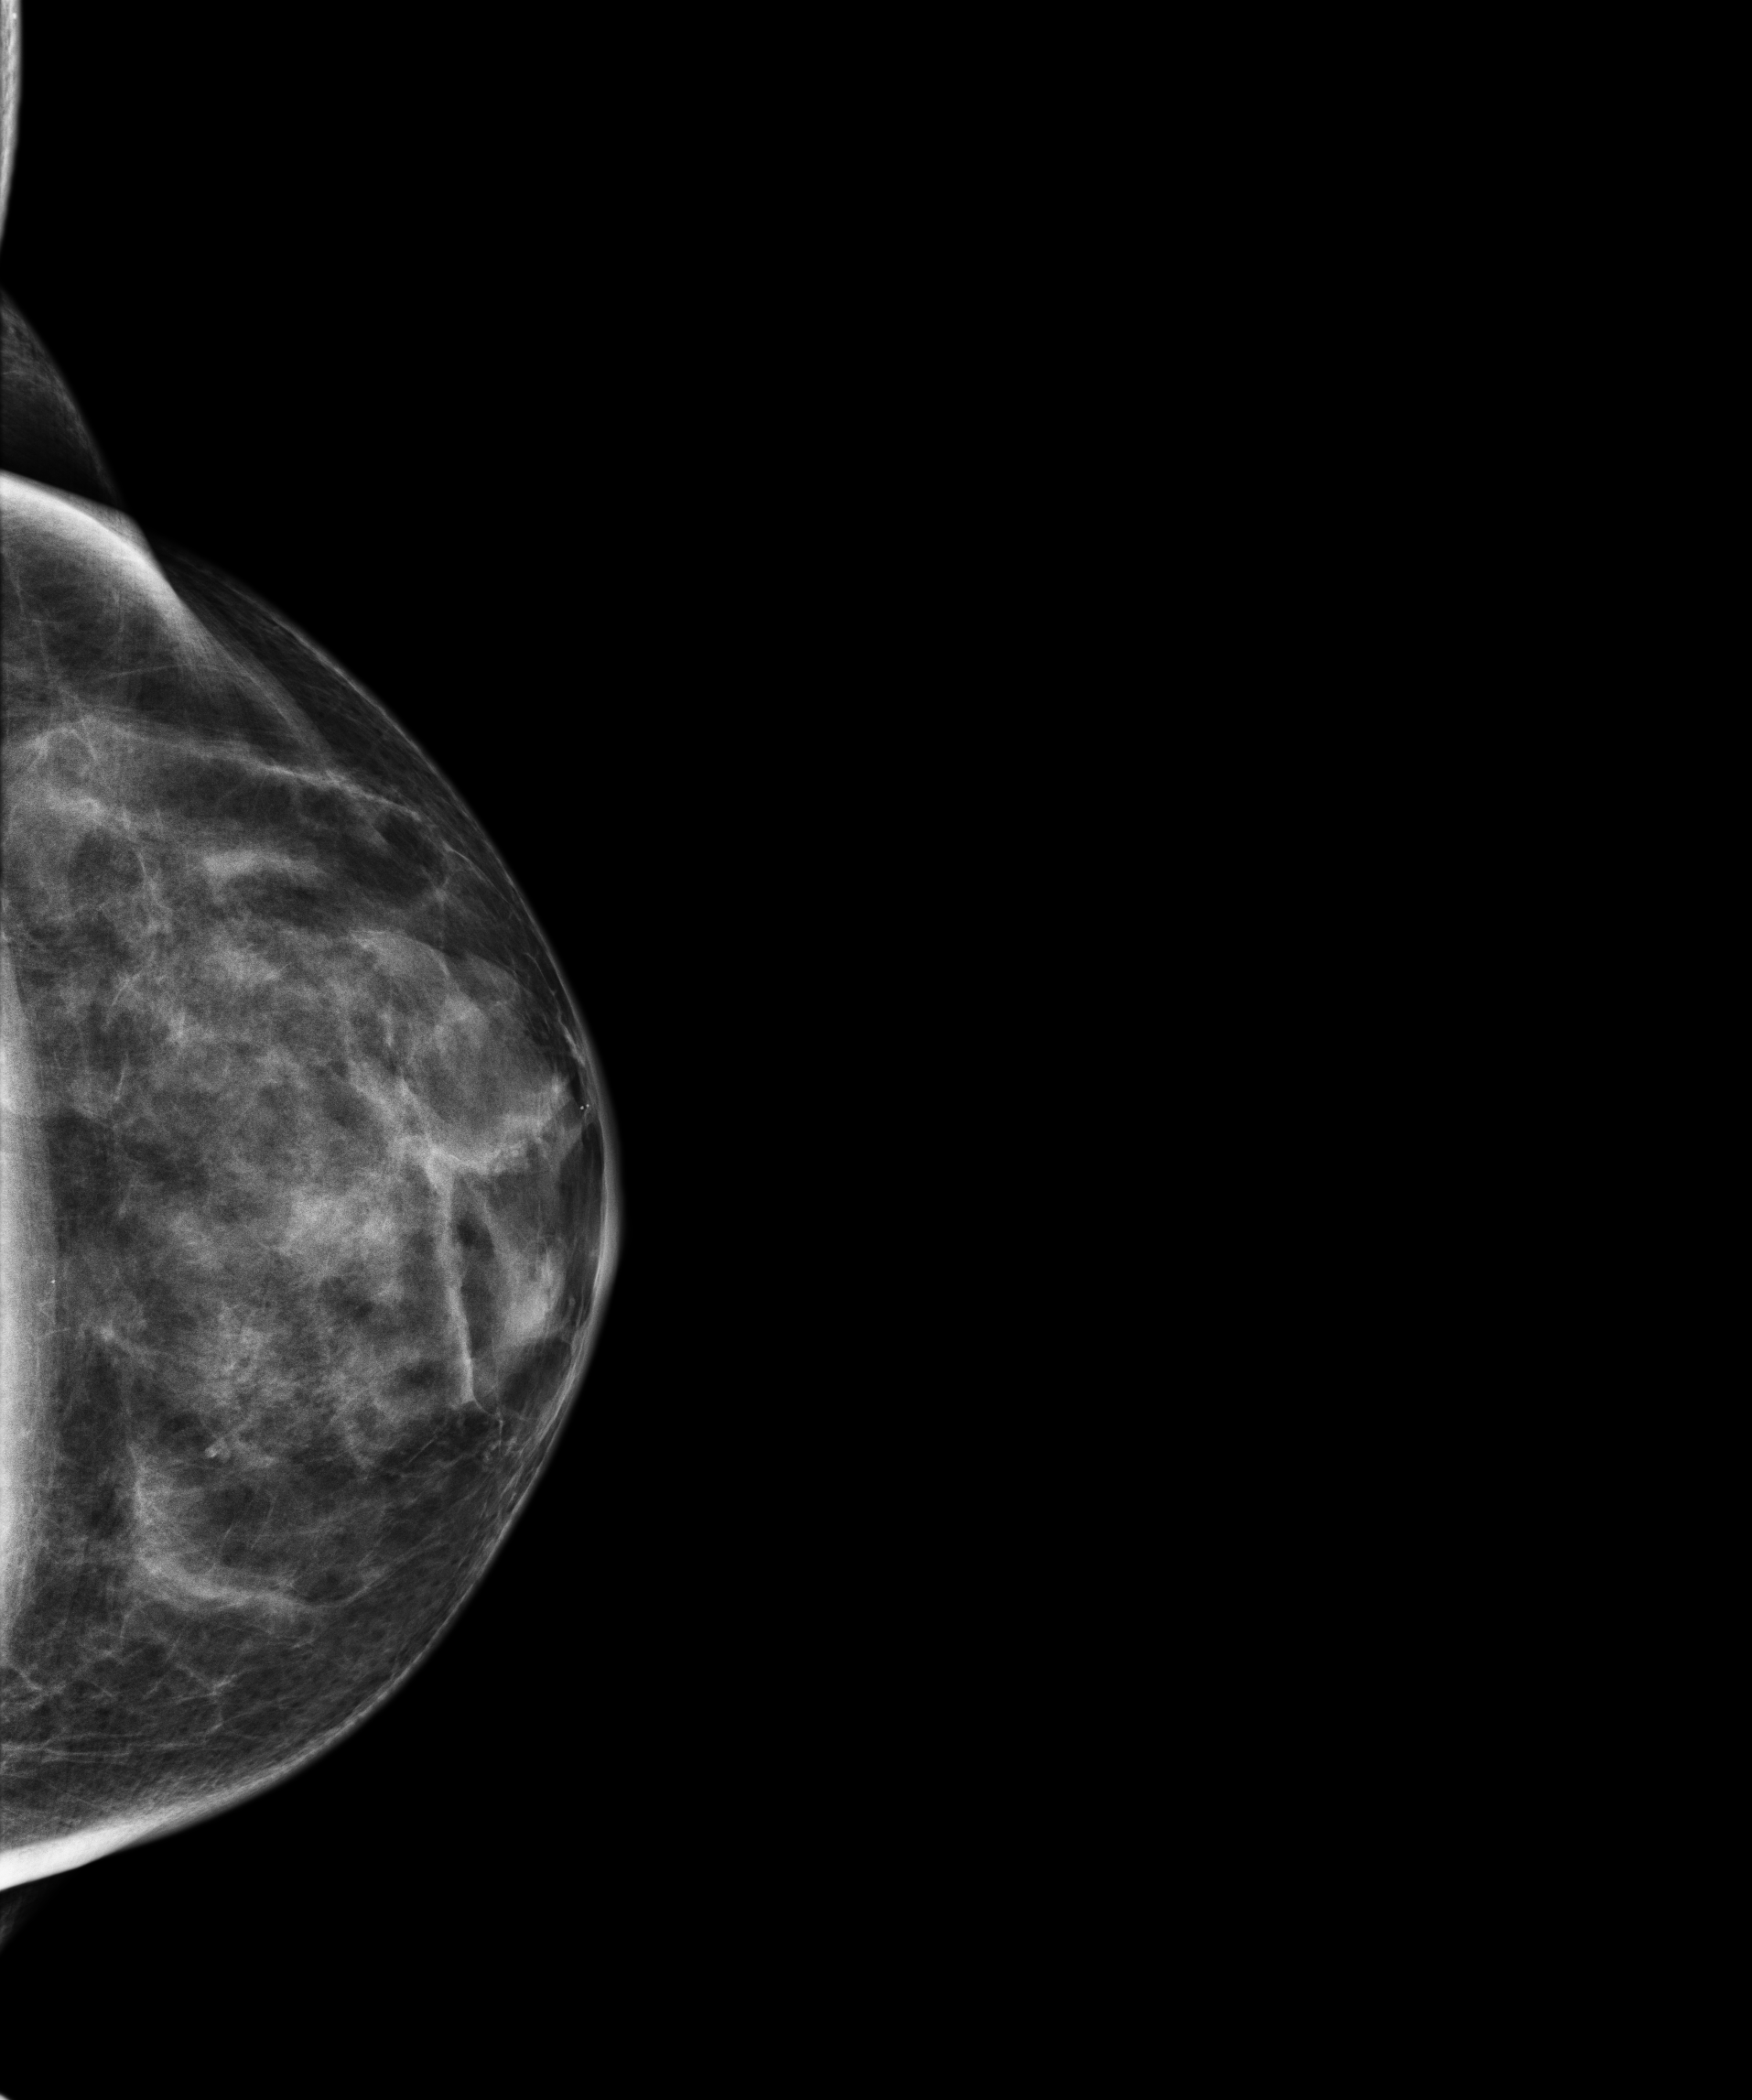
Annual screening mammography examination, compressed breast thickness 60 mm, system: Senographe Essential ADS_56.21.3. Female patient, age 67 years.
Image type: full-field digital mammogram. Breast: left. Projection: craniocaudal (CC) view.